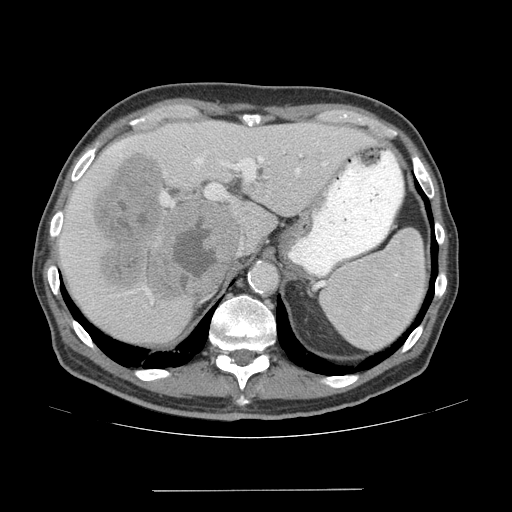
Contrast-enhanced abdominal CT (liver protocol), one axial slice. Slice 46 of 77 in the series (ordered by position). Reconstruction kernel STANDARD. Soft-tissue window (W 400 / L 40 HU). 2.5 mm slice thickness. 512 × 512 image matrix, field of view 400 × 400 mm. From the clinical record (not read from this slice): diagnosis: hepatocellular carcinoma (patient treated with transarterial chemoembolisation; whether this scan precedes or follows treatment is not stated here); TNM stage (as recorded): Stage-IVA; Child-Pugh class: A; tumour differentiation: well differentiated; tumour nodularity: uninodular.
Structures marked on this image (semi-automatic segmentation, software-assisted and operator-edited):
- liver parenchyma outside the tumour (the mass and vessels are separate outlines, so this box may not span the whole liver): bounding box (x1, y1, x2, y2) in pixels: (58, 120, 372, 342)
- mass: (93, 152, 239, 299)
- liver vessels: (106, 139, 328, 304)